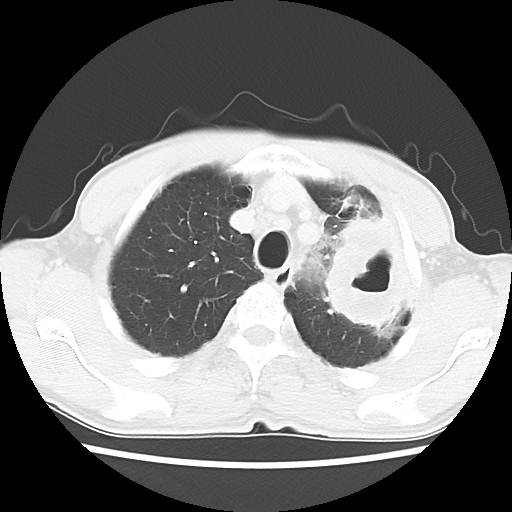
Chest CT, one axial slice. Reconstruction kernel LUNG. 120 kVp. Lung window (W 1500 / L -600 HU). 5 mm slice thickness. 512 × 512 image matrix, field of view 308 × 308 mm. Patient: male, 64 years. Case-level facts recorded for this patient, not image findings: clinical TNM (as recorded): T3 N3 M0.
Outlined on this slice (bounding box drawn by a radiologist):
- lung tumour (recorded histology: adenocarcinoma): bounding box [x1, y1, x2, y2] px = [316, 203, 419, 343]